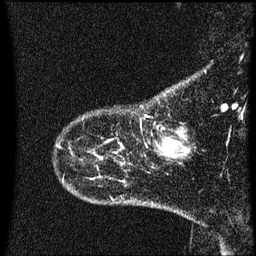
Breast MRI (dynamic contrast-enhanced), one sagittal slice; slice 7 of 60 in the series (ordered by position); dynamic contrast-enhanced series, image 2 of 3 at this slice position (ordered by acquisition); 1.5 T; TE 4.2 ms, TR 8.4 ms; 2 mm slice thickness; 256 × 256 image matrix, field of view 200 × 200 mm. Female patient, age 41 years. From the clinical record (not read from this slice): setting: breast cancer imaged before/during neoadjuvant chemotherapy; receptor status: triple-negative.
Outlined on this slice (semi-automatic segmentation, software-assisted and operator-edited):
- analysis volume of interest (the breast-tissue region the enhancement analysis was run in; not a lesion): bounding box [x1, y1, x2, y2] px = [165, 138, 176, 157]
- tumour enhancement mask (voxels above the 70 % enhancement threshold inside the analysis volume of interest): [166, 142, 169, 147]